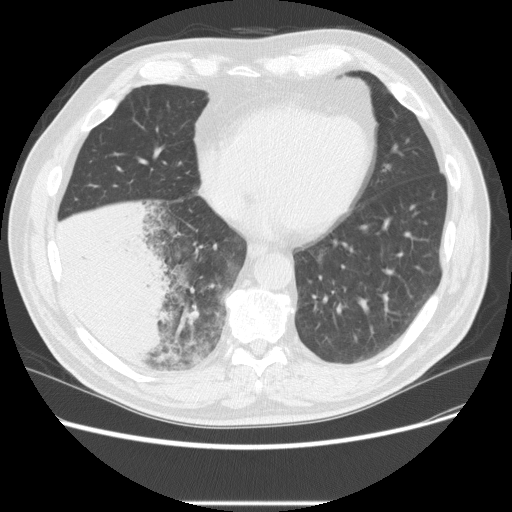
Low-dose screening chest CT, one axial slice; position 78 of 233 along the scan axis; lung window (W 1500 / L -600 HU); 2.5 mm slice thickness; 512 × 512 image matrix, field of view 380 × 380 mm.
Structures marked on this image (expert manual segmentation):
- lesion 3 (tumor, lower lobe of right lung): box from (x=54, y=201) to (x=176, y=366) px